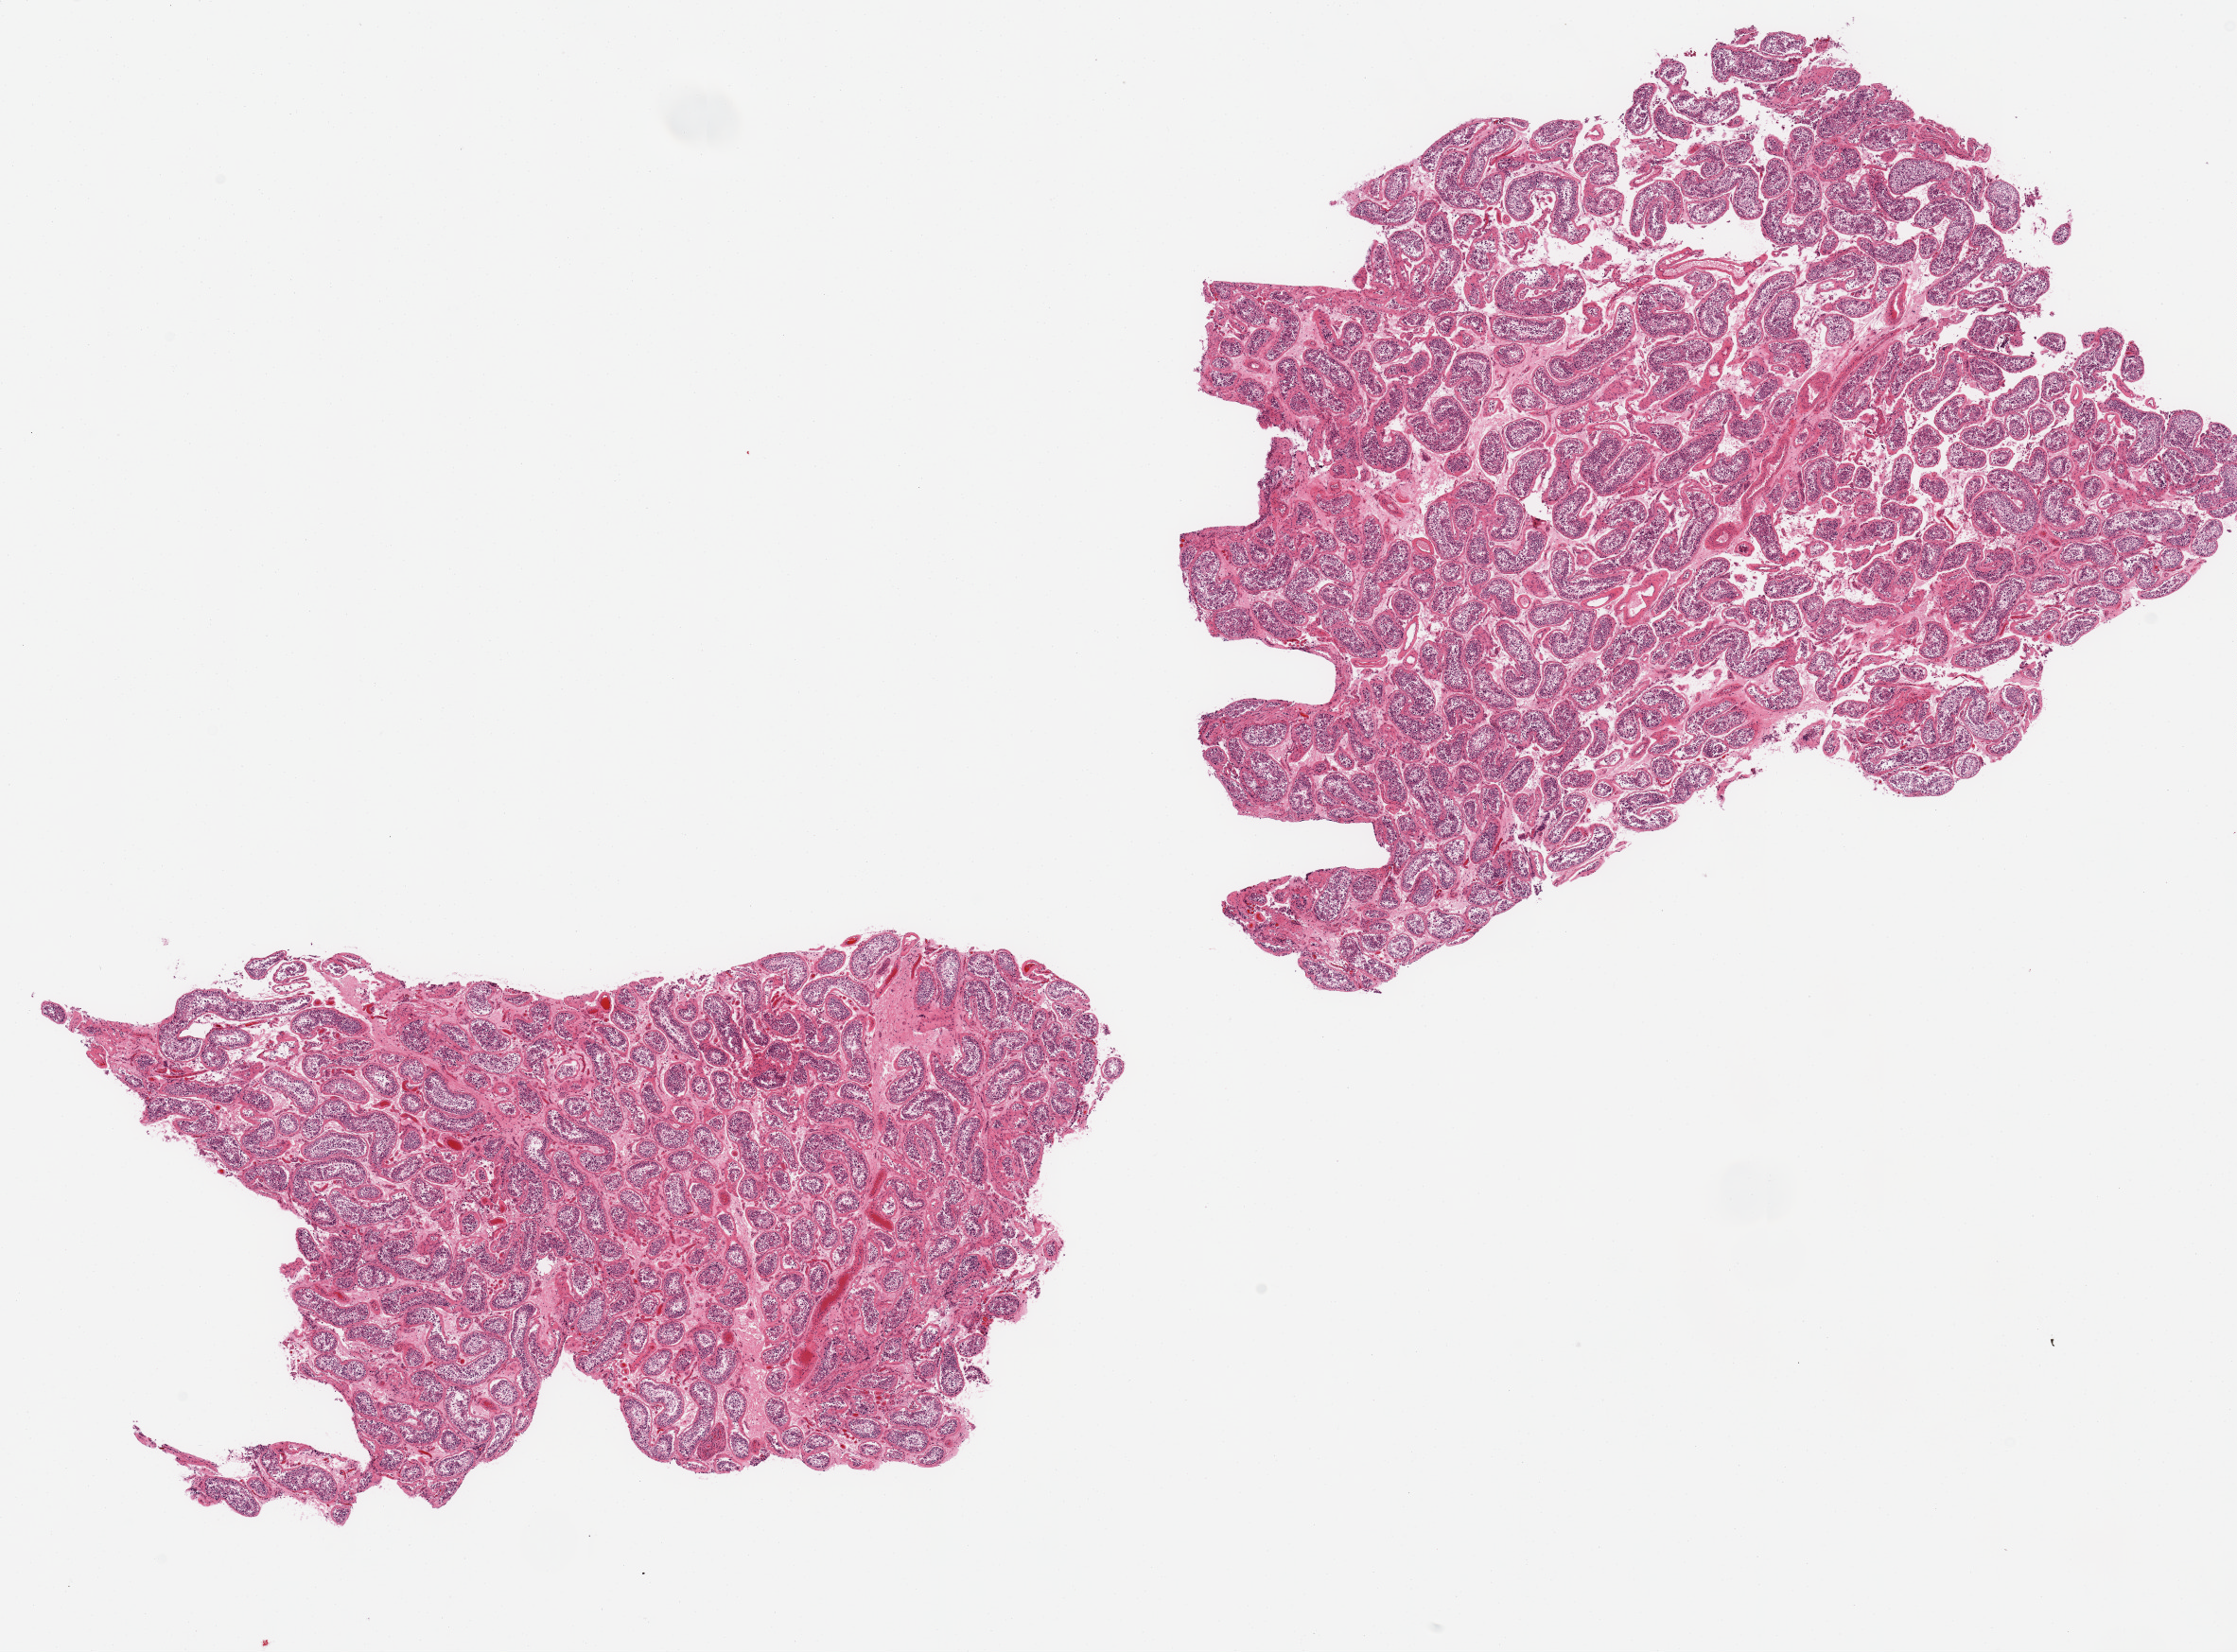
Haematoxylin and eosin whole-slide image, a low-resolution overview of the entire scanned area, about 18.7 x 13.8 mm; PAXgene-fixed, paraffin-embedded tissue; section of testis (target tissue); donor tissue sample. Male donor.
- review note (as recorded): 2 pieces; spermatogenesis present